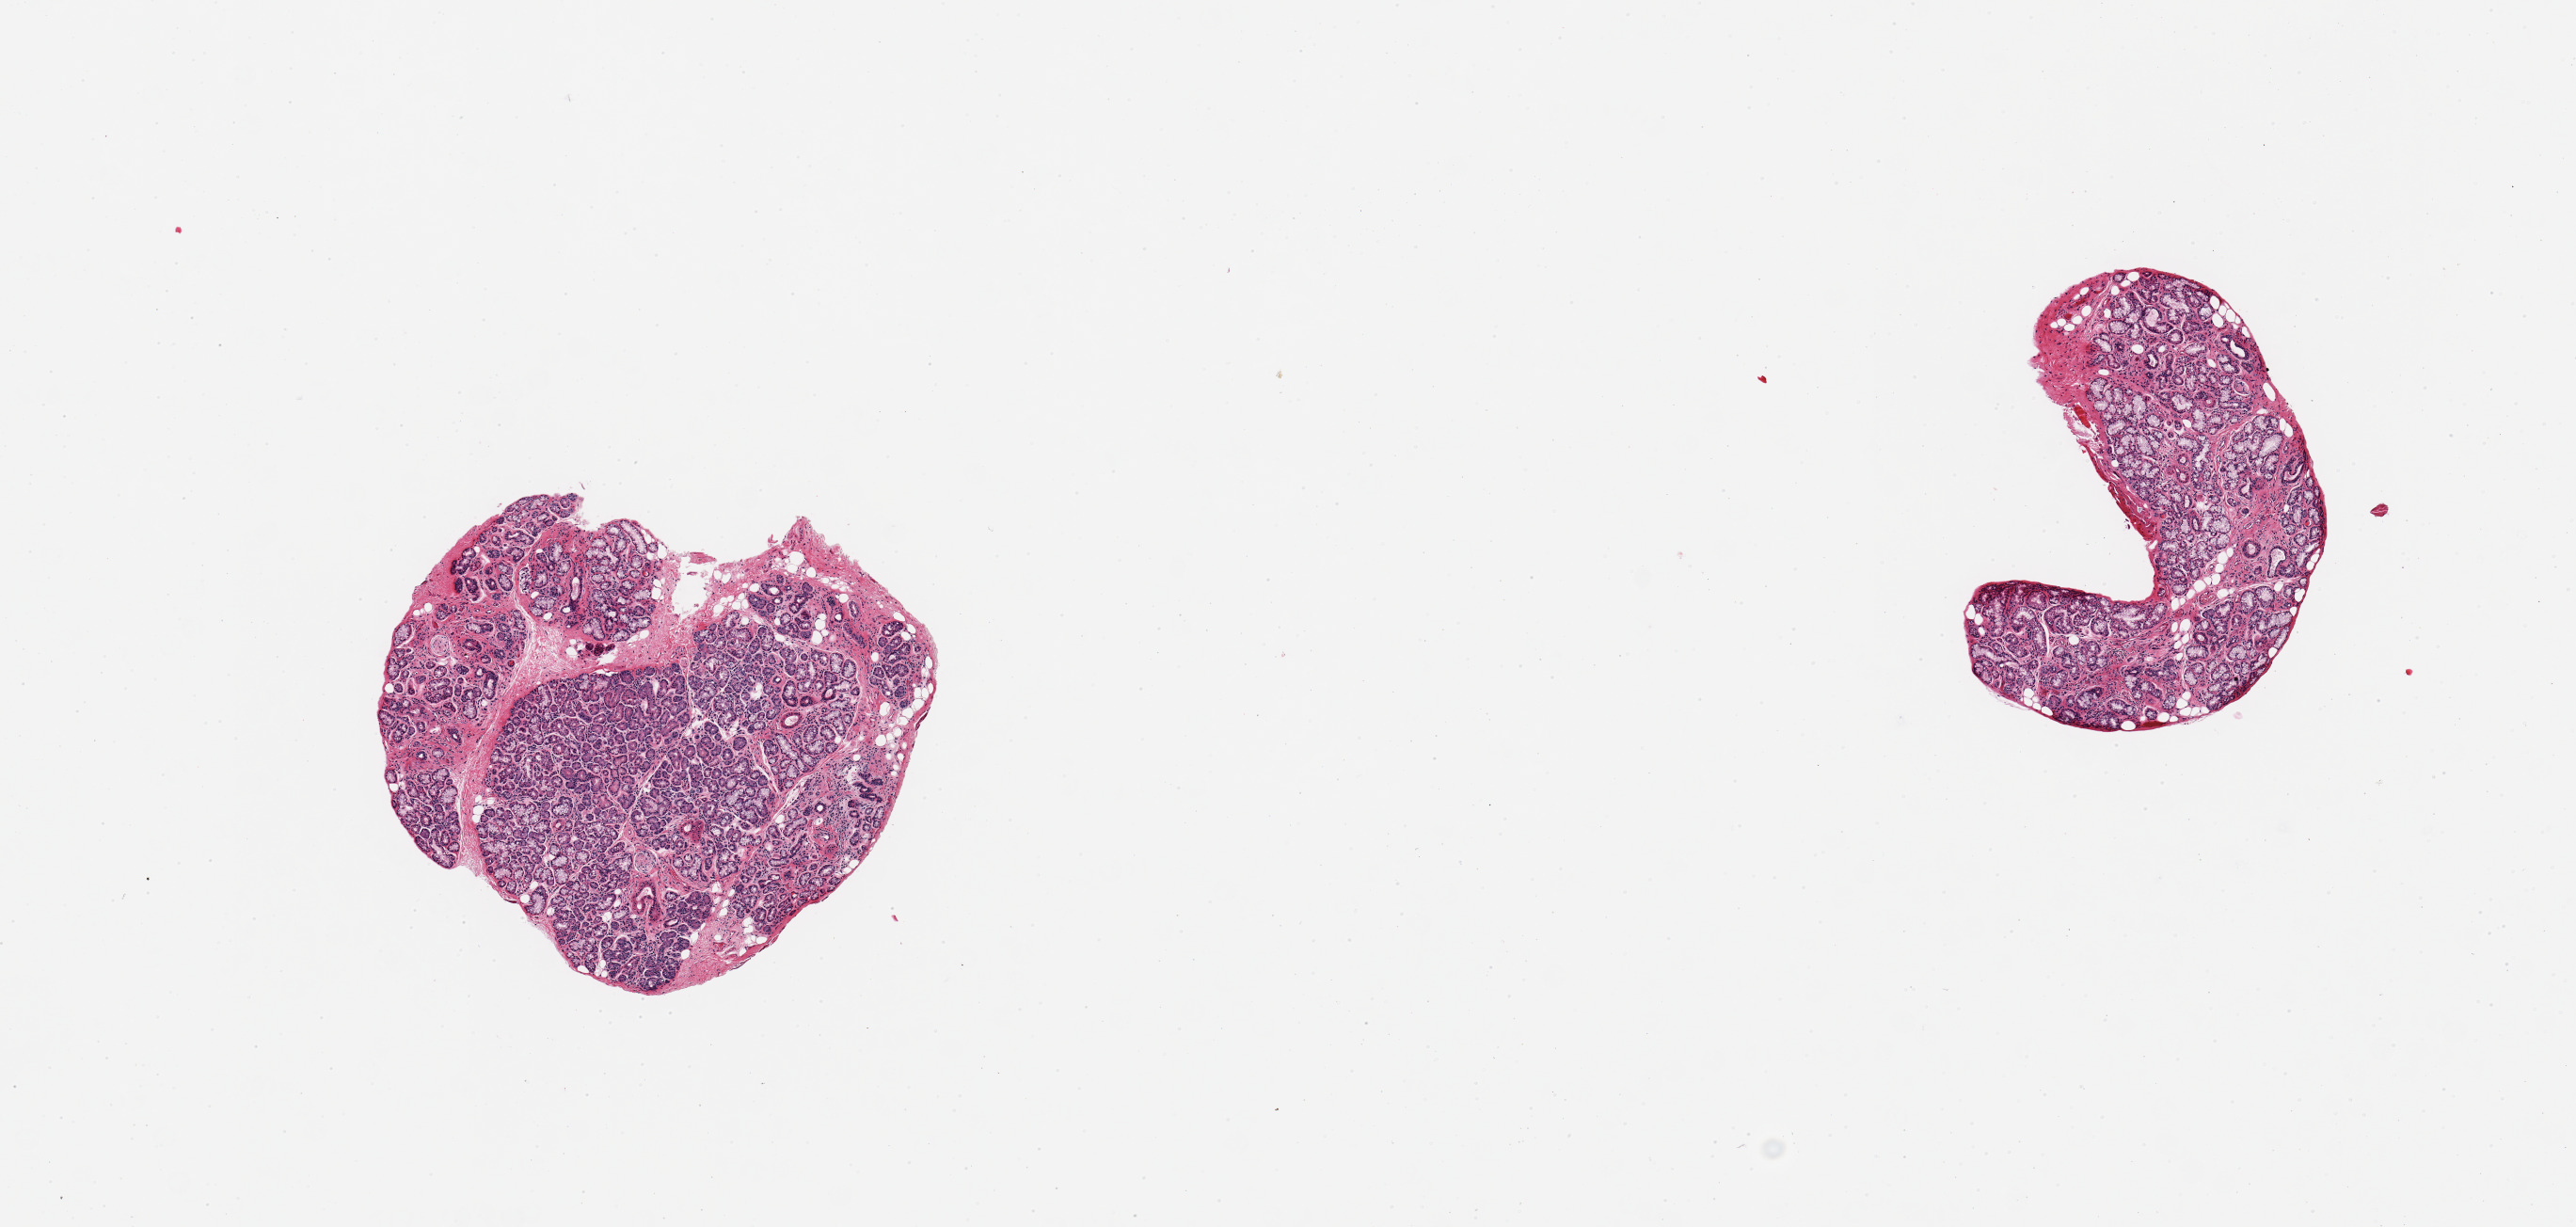
Digitized haematoxylin and eosin-stained section, brightfield, whole scanned area (about 10.8 x 5.2 mm, acquisition: 20x scan) shown as a low-resolution overview; PAXgene-fixed, paraffin-embedded tissue; section of minor salivary gland (target tissue); tissue donor sample.
Pathologist's review note for this sample: 2 pieces, glandular parenchyma is ~95% of specimen, trace adherent fibrous nubbin up to 0.2mm.